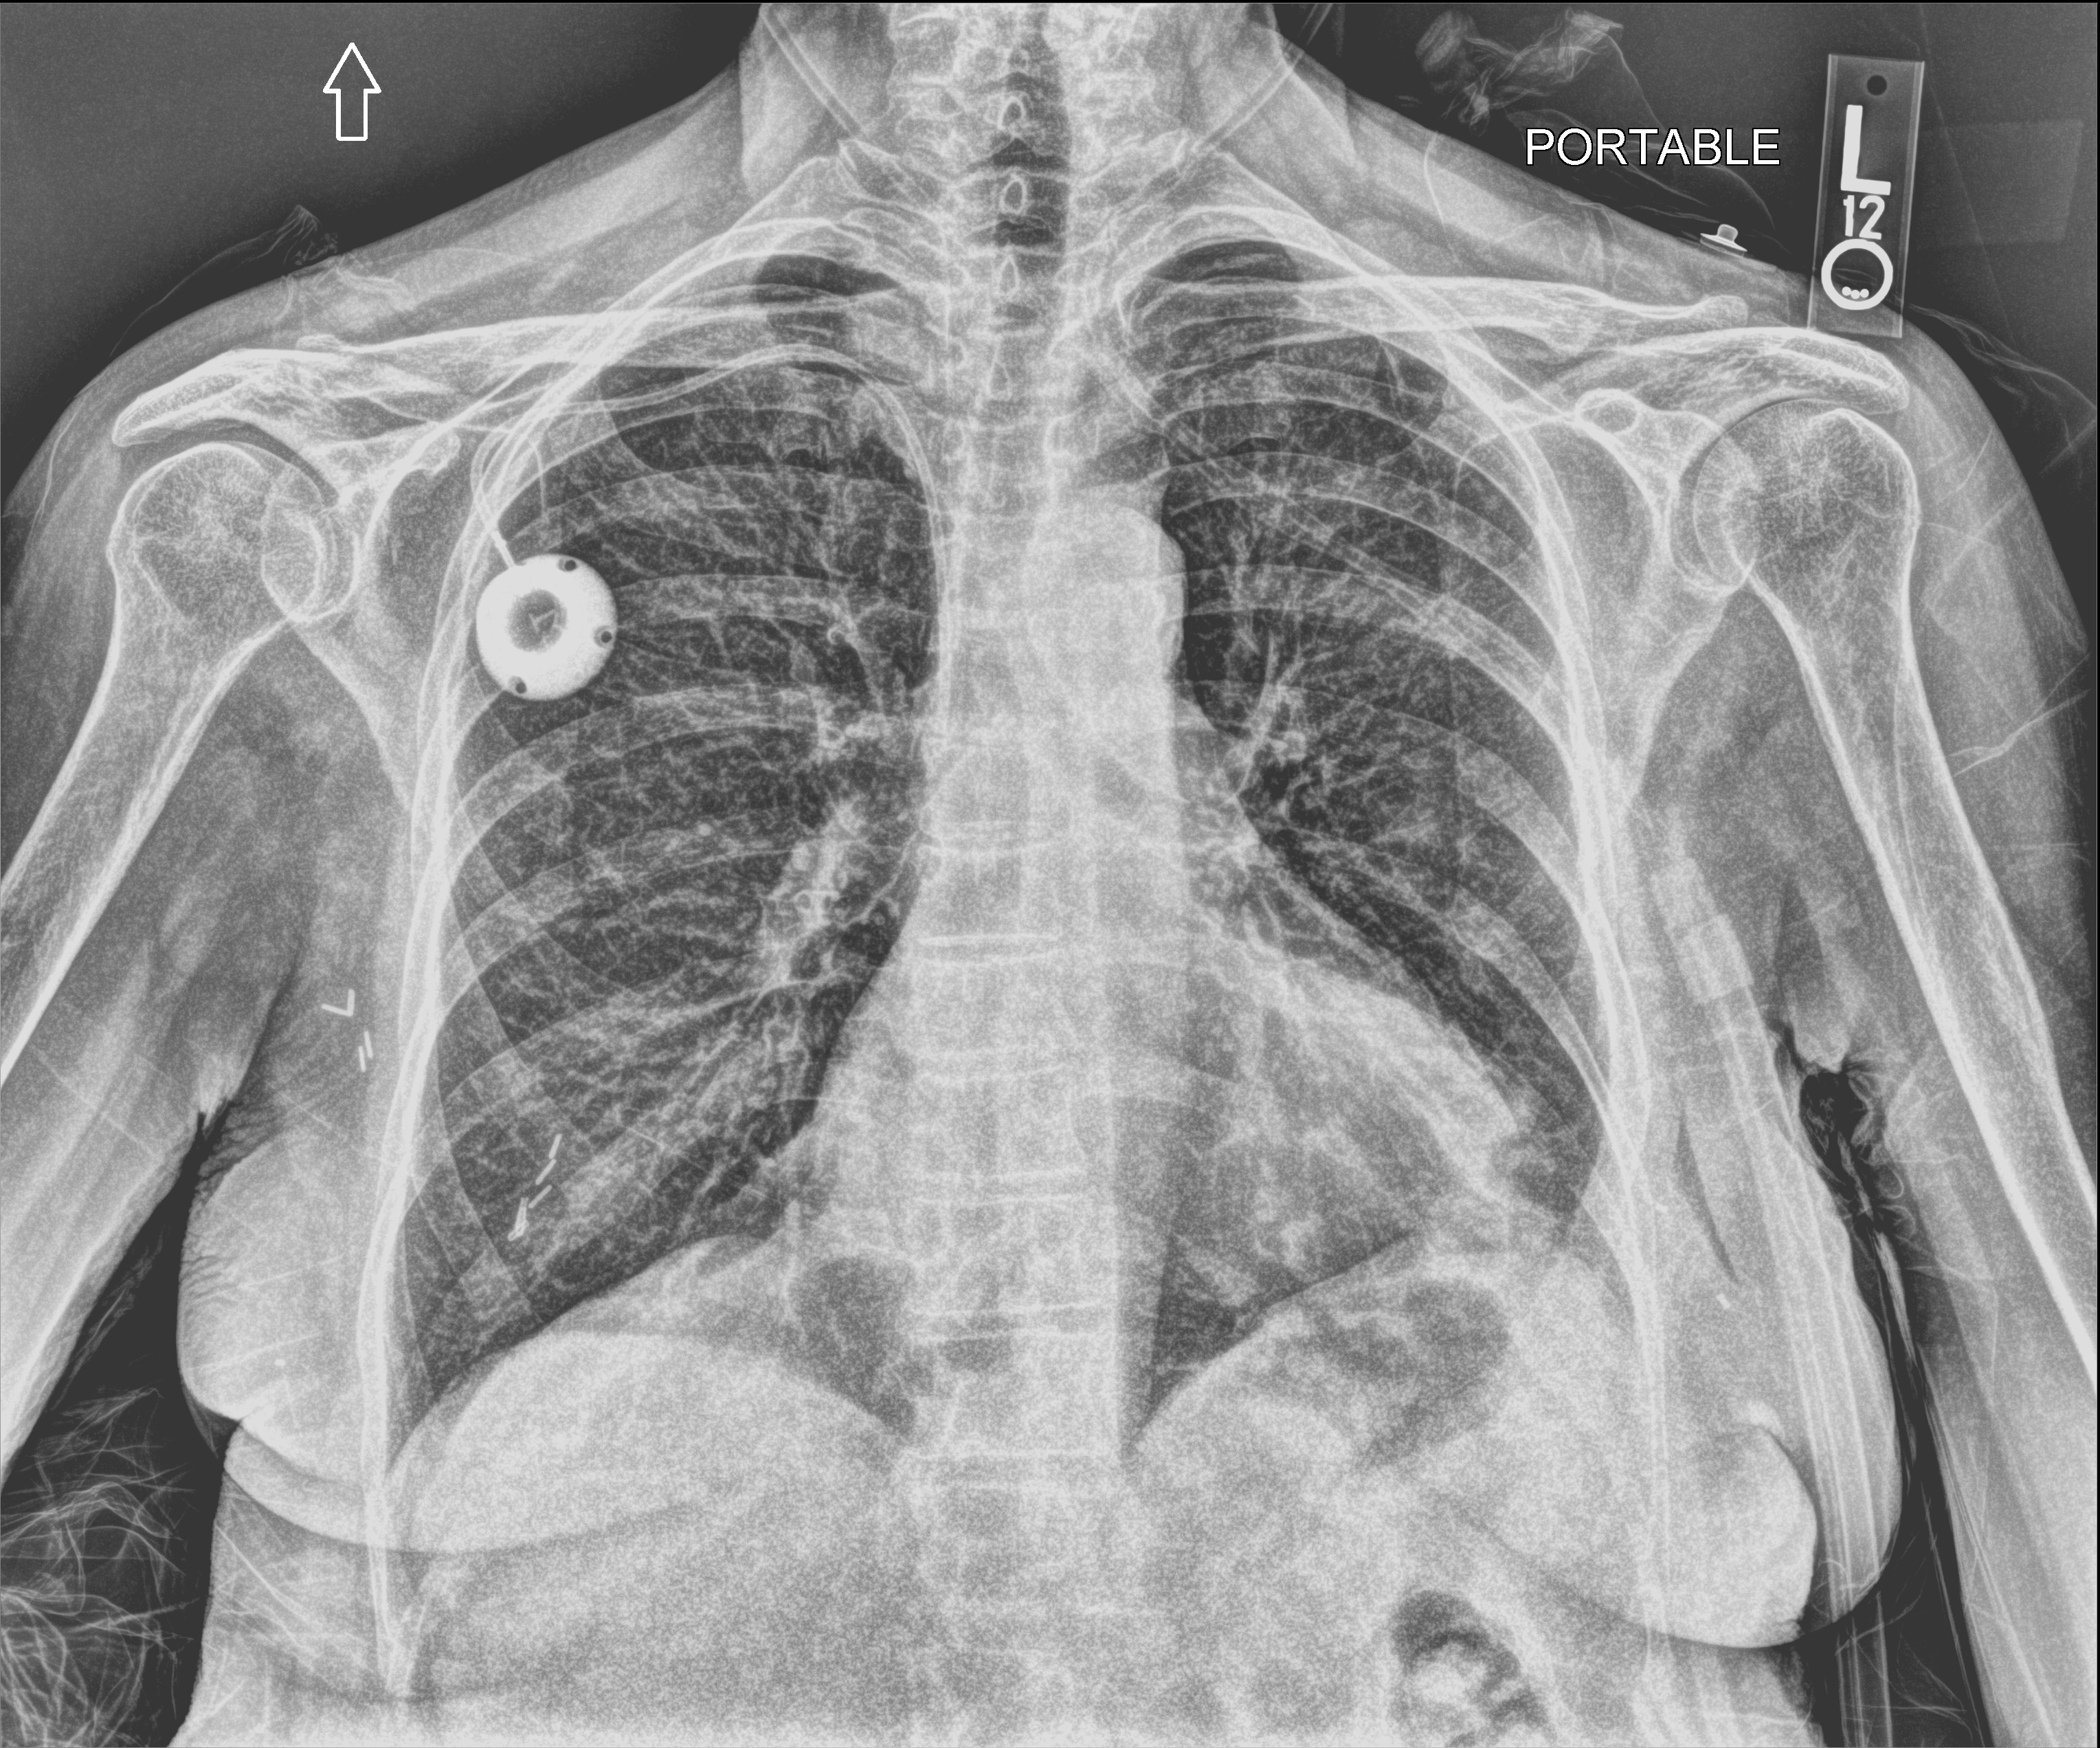
Bedside chest radiograph (computed radiography); anteroposterior (AP) projection. Female patient hospitalised with COVID-19, age 60–74 years.
Admission-level facts for this patient (not findings on this image; timing relative to this image not recorded):
- admitted to intensive care during this hospital stay: yes
- COPD (admission record): no